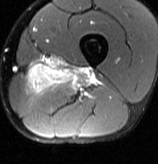
MRI of an extremity soft-tissue mass, one axial slice; position 23 of 70 along the scan axis; T2-weighted fat-saturated; MR volume resampled by the dataset authors to the PET/CT grid (not the native acquisition matrix); 158 × 164 image matrix. Male patient. Case-level facts recorded for this patient, not image findings: histological type: extraskeletal osteosarcoma; grade: high; site of the primary tumour: left adductur.
Outlined on this slice (expert contour drawn on MRI and transferred to this co-registered scan by the dataset authors):
- gross tumour volume (mass): bounding box <24,64,98,92> (left, top, right, bottom; pixels)